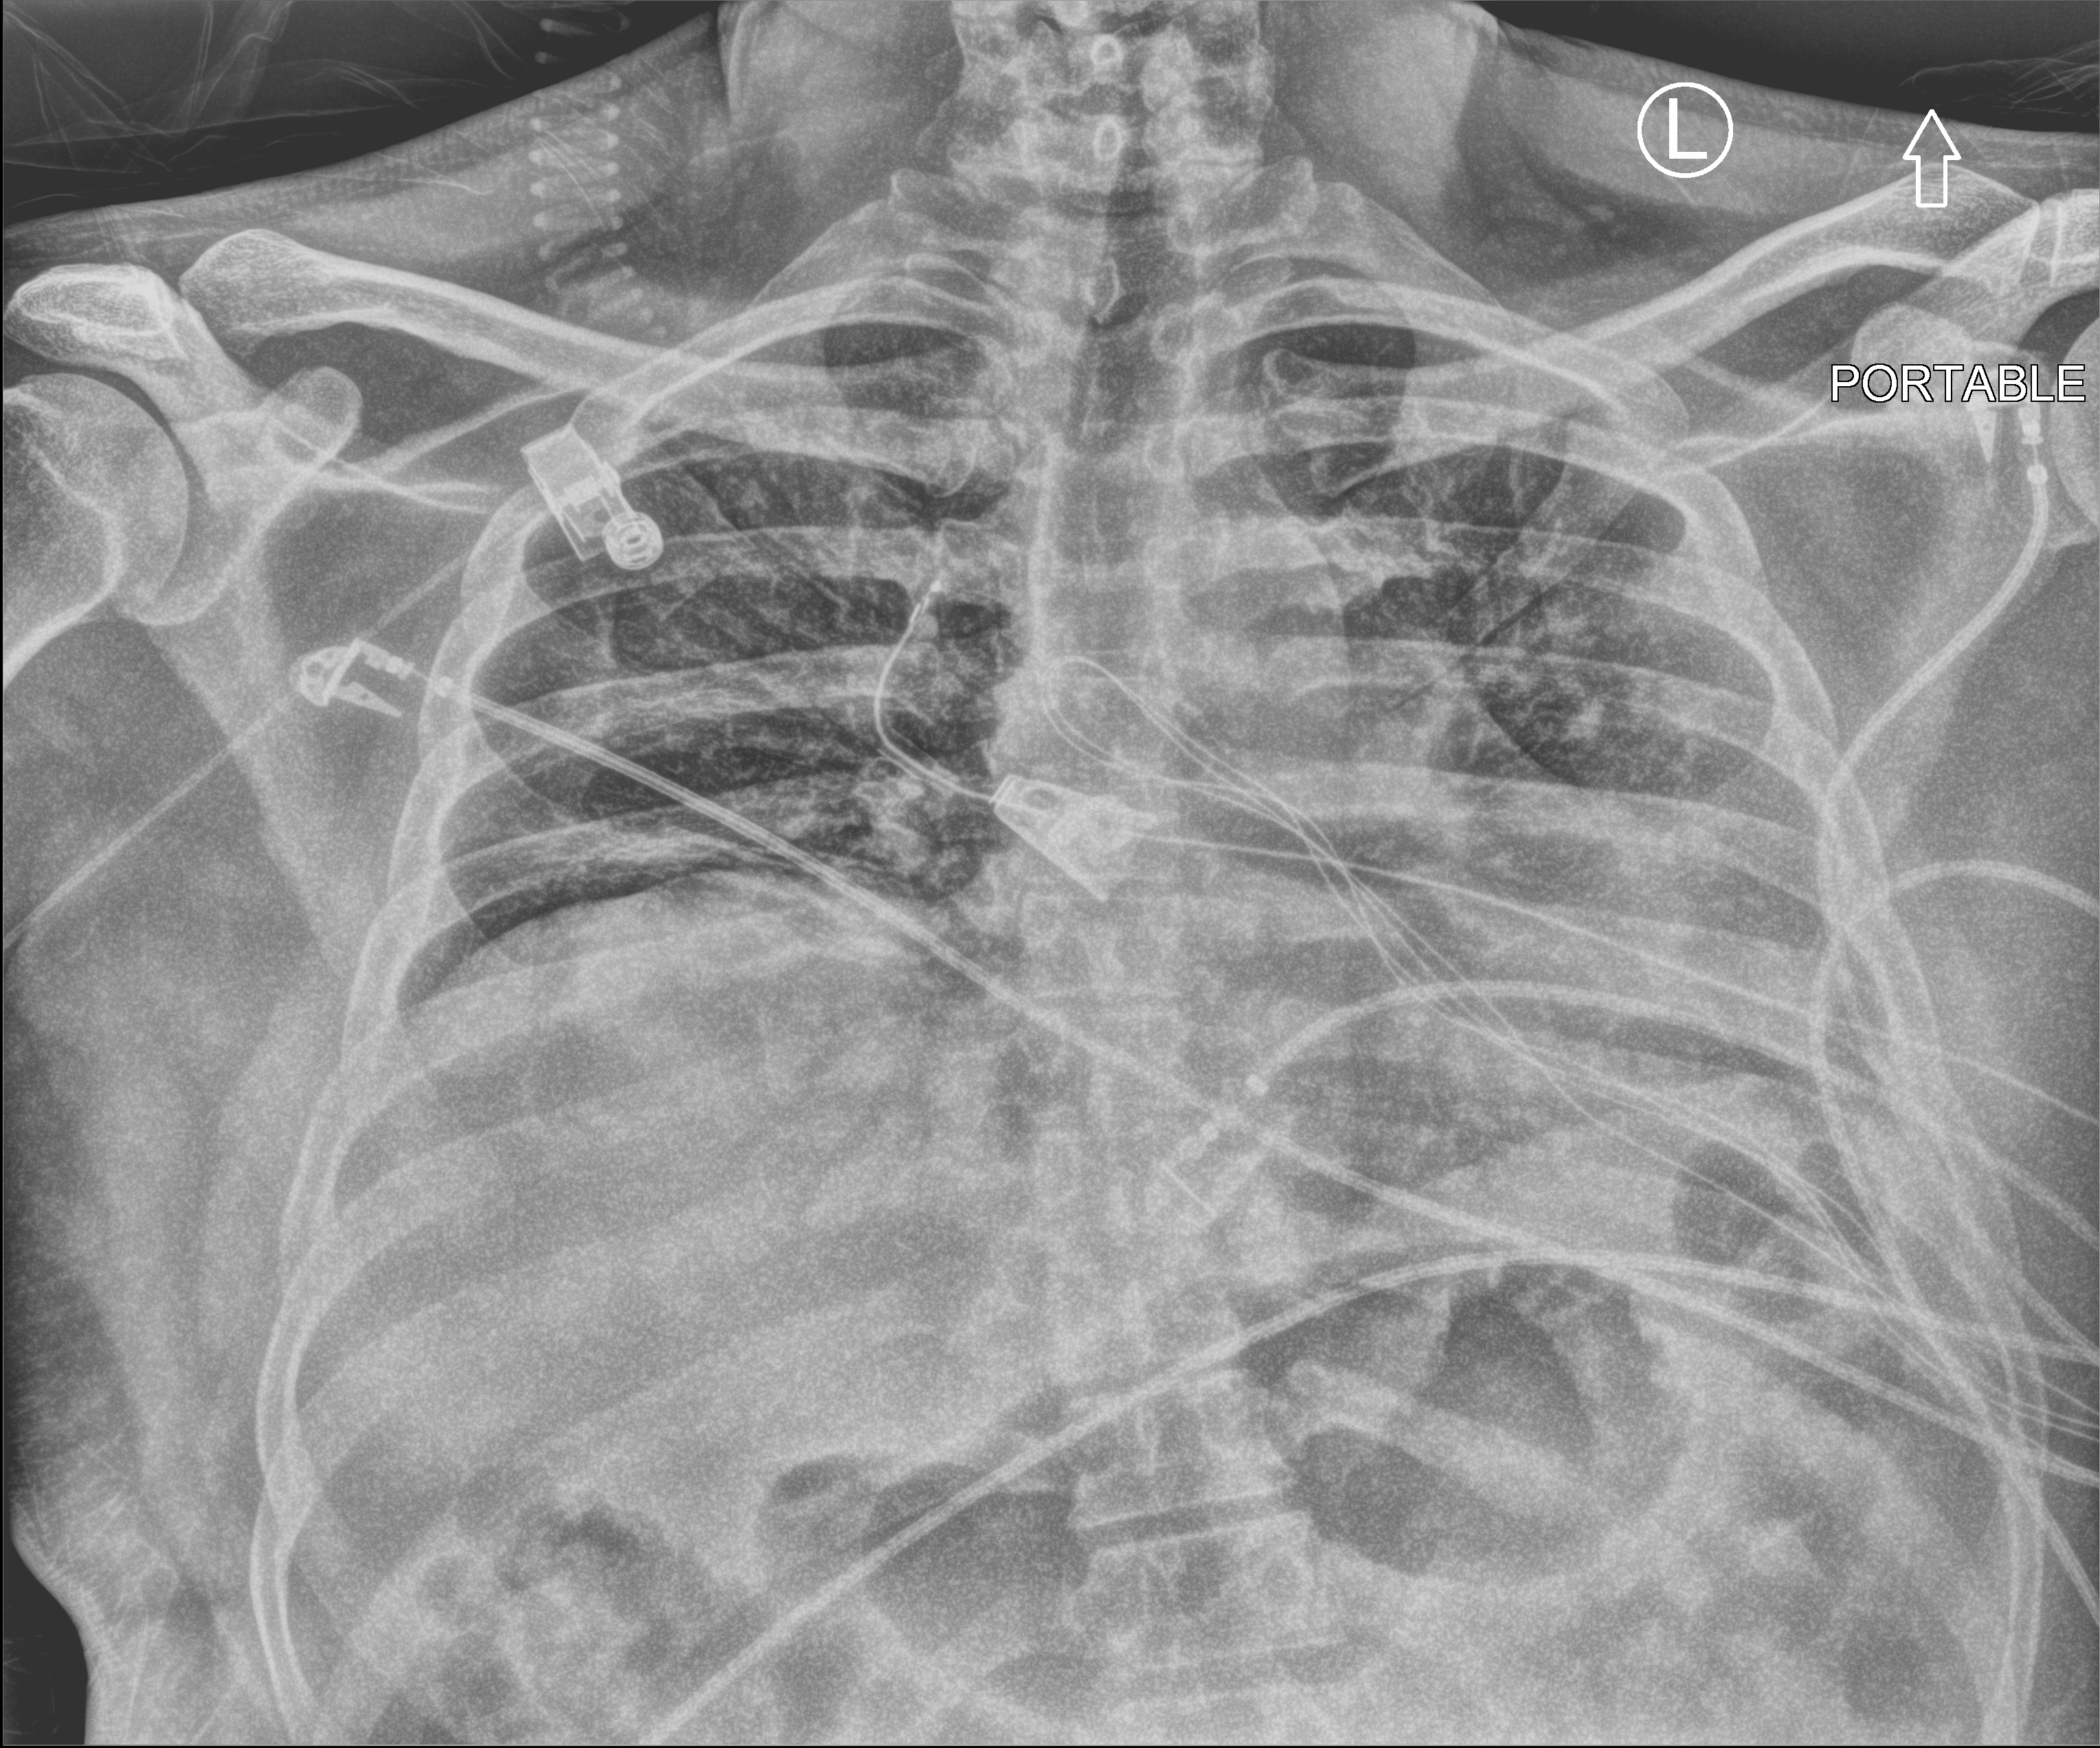
Portable chest radiograph; anteroposterior (AP) projection. Patient hospitalised with COVID-19; male, aged 18–59 years.
Admission-level facts for this patient (not findings on this image; timing relative to this image not recorded):
- admitted to intensive care during this hospital stay: yes